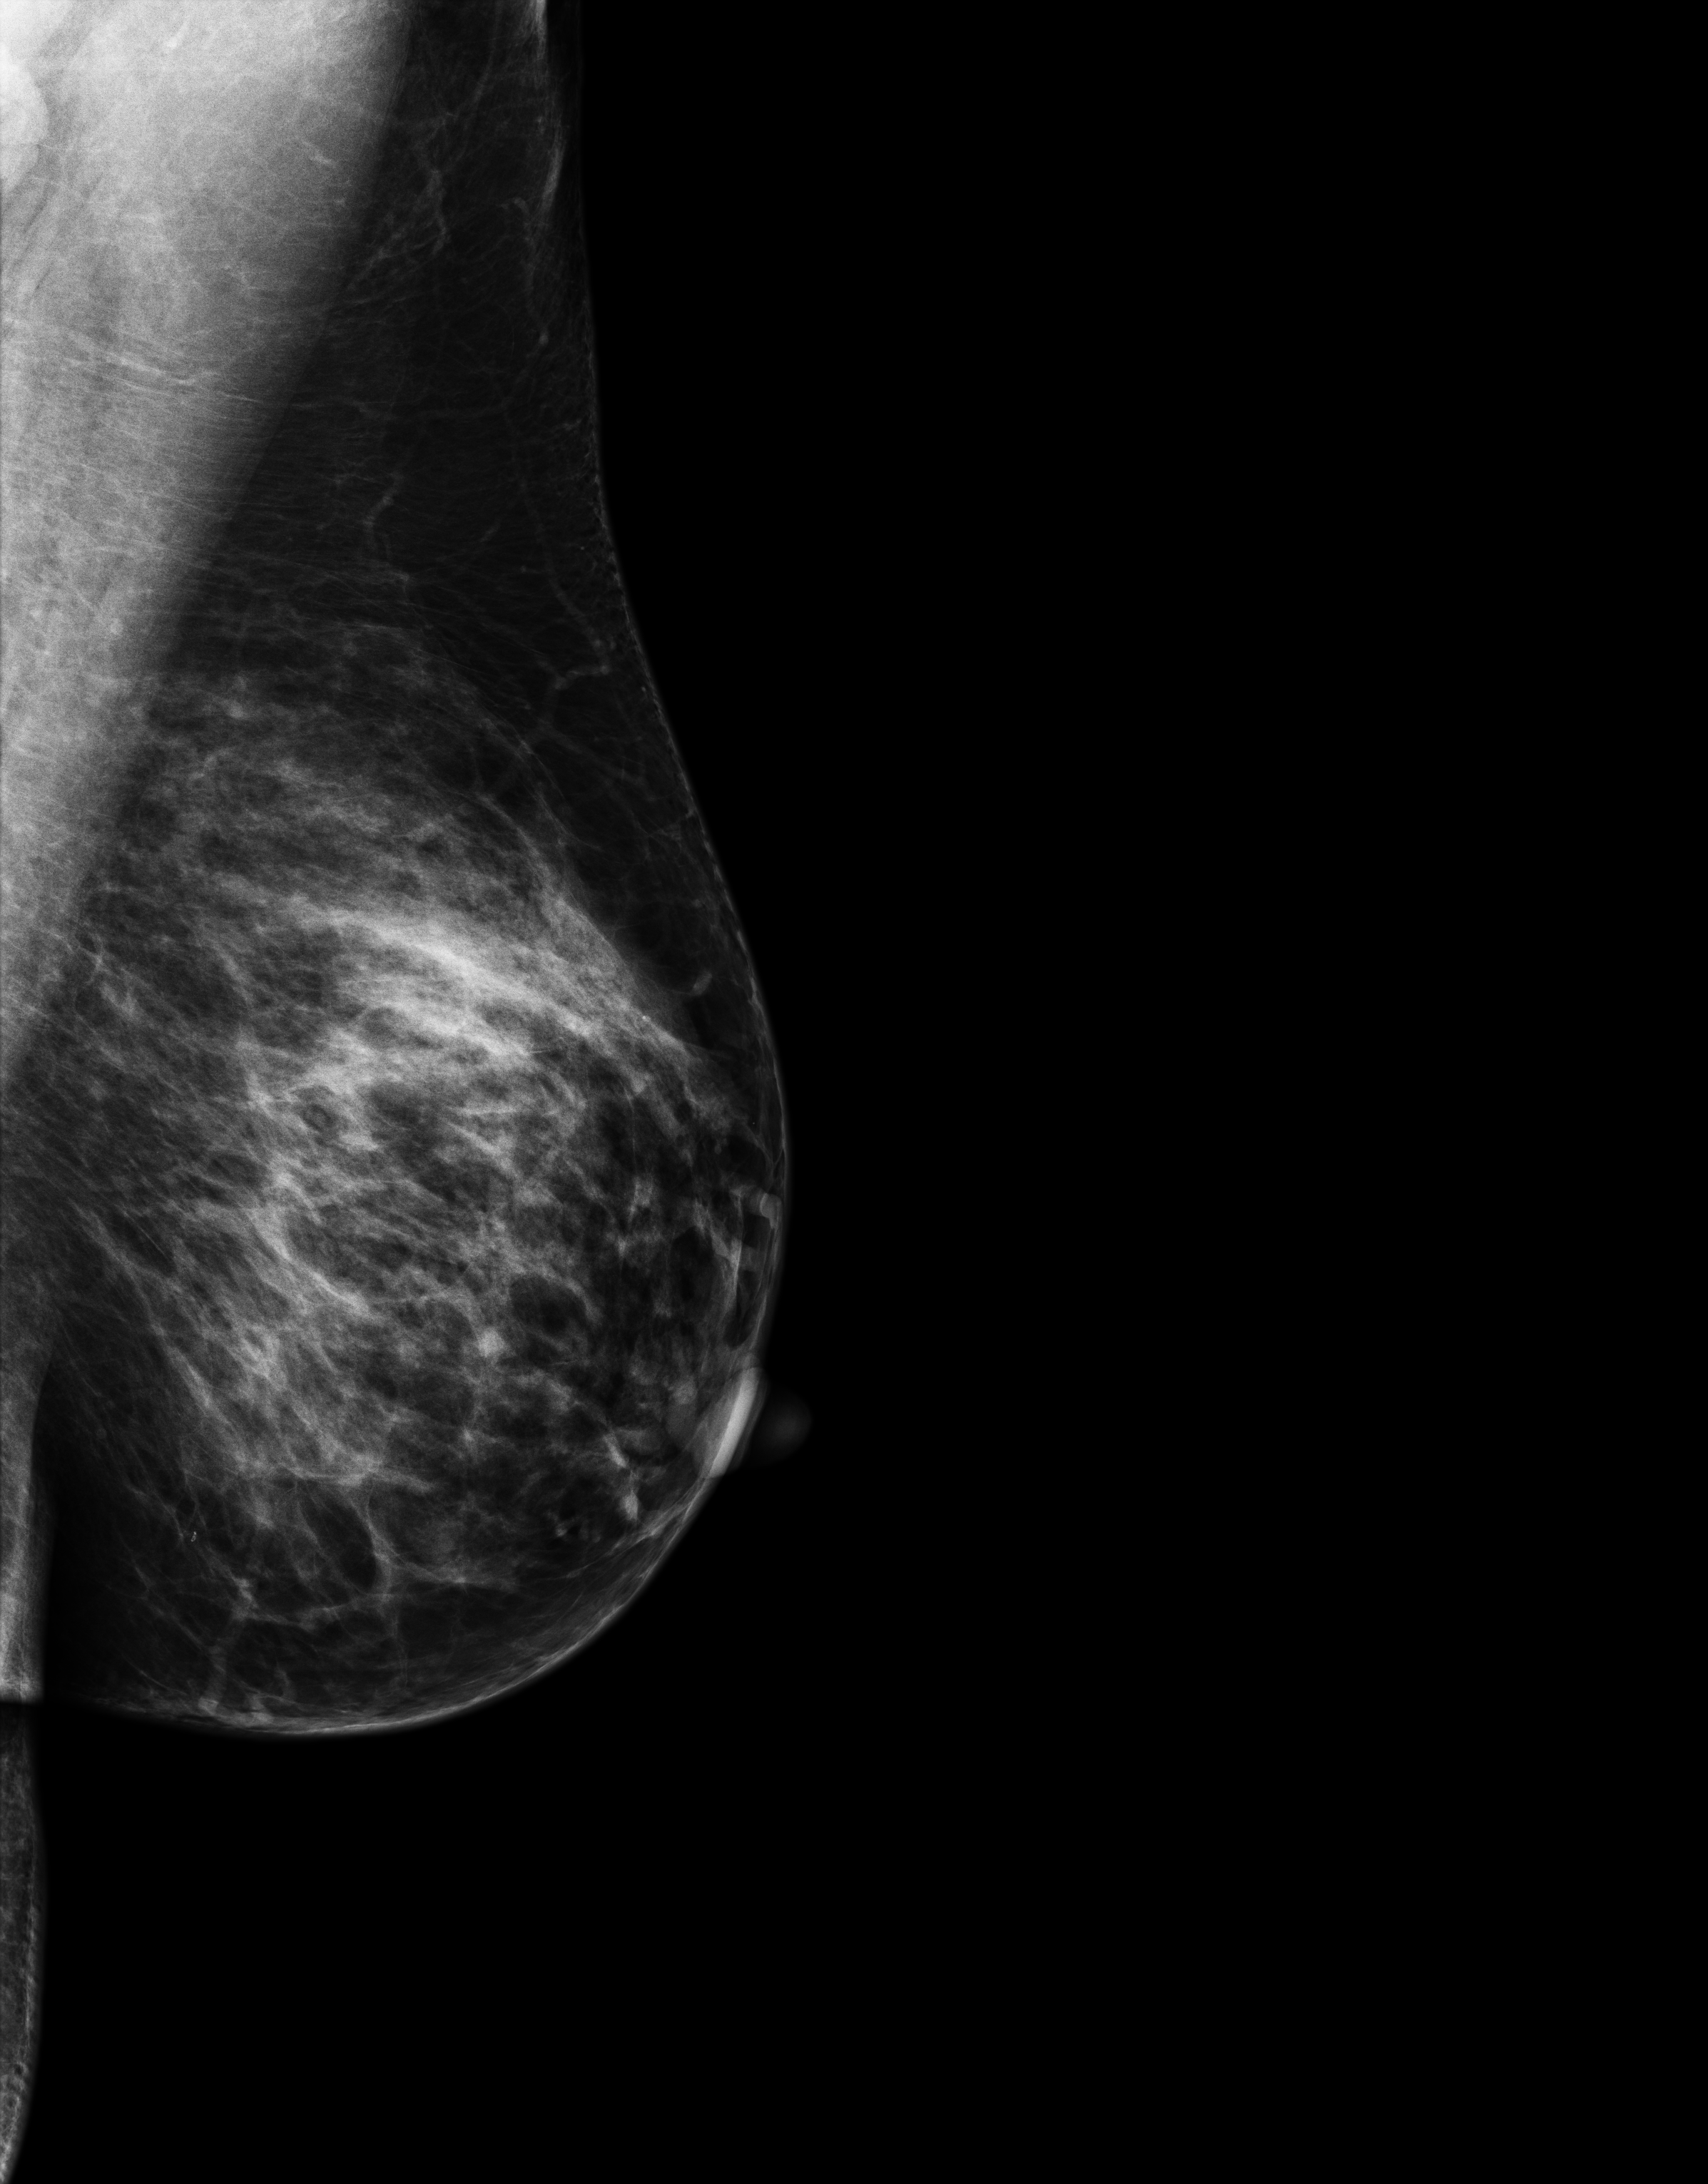
Digital mammogram (FFDM); left breast; MLO view; annual screening mammography examination; compressed breast thickness 76 mm. Patient: female, 49 years.
- BI-RADS breast density category at the screening exam (both breasts, scale 1–4): 3
- final BI-RADS category for the screening round (tomosynthesis exam, both breasts): category 1
- recall: no recall after this screen